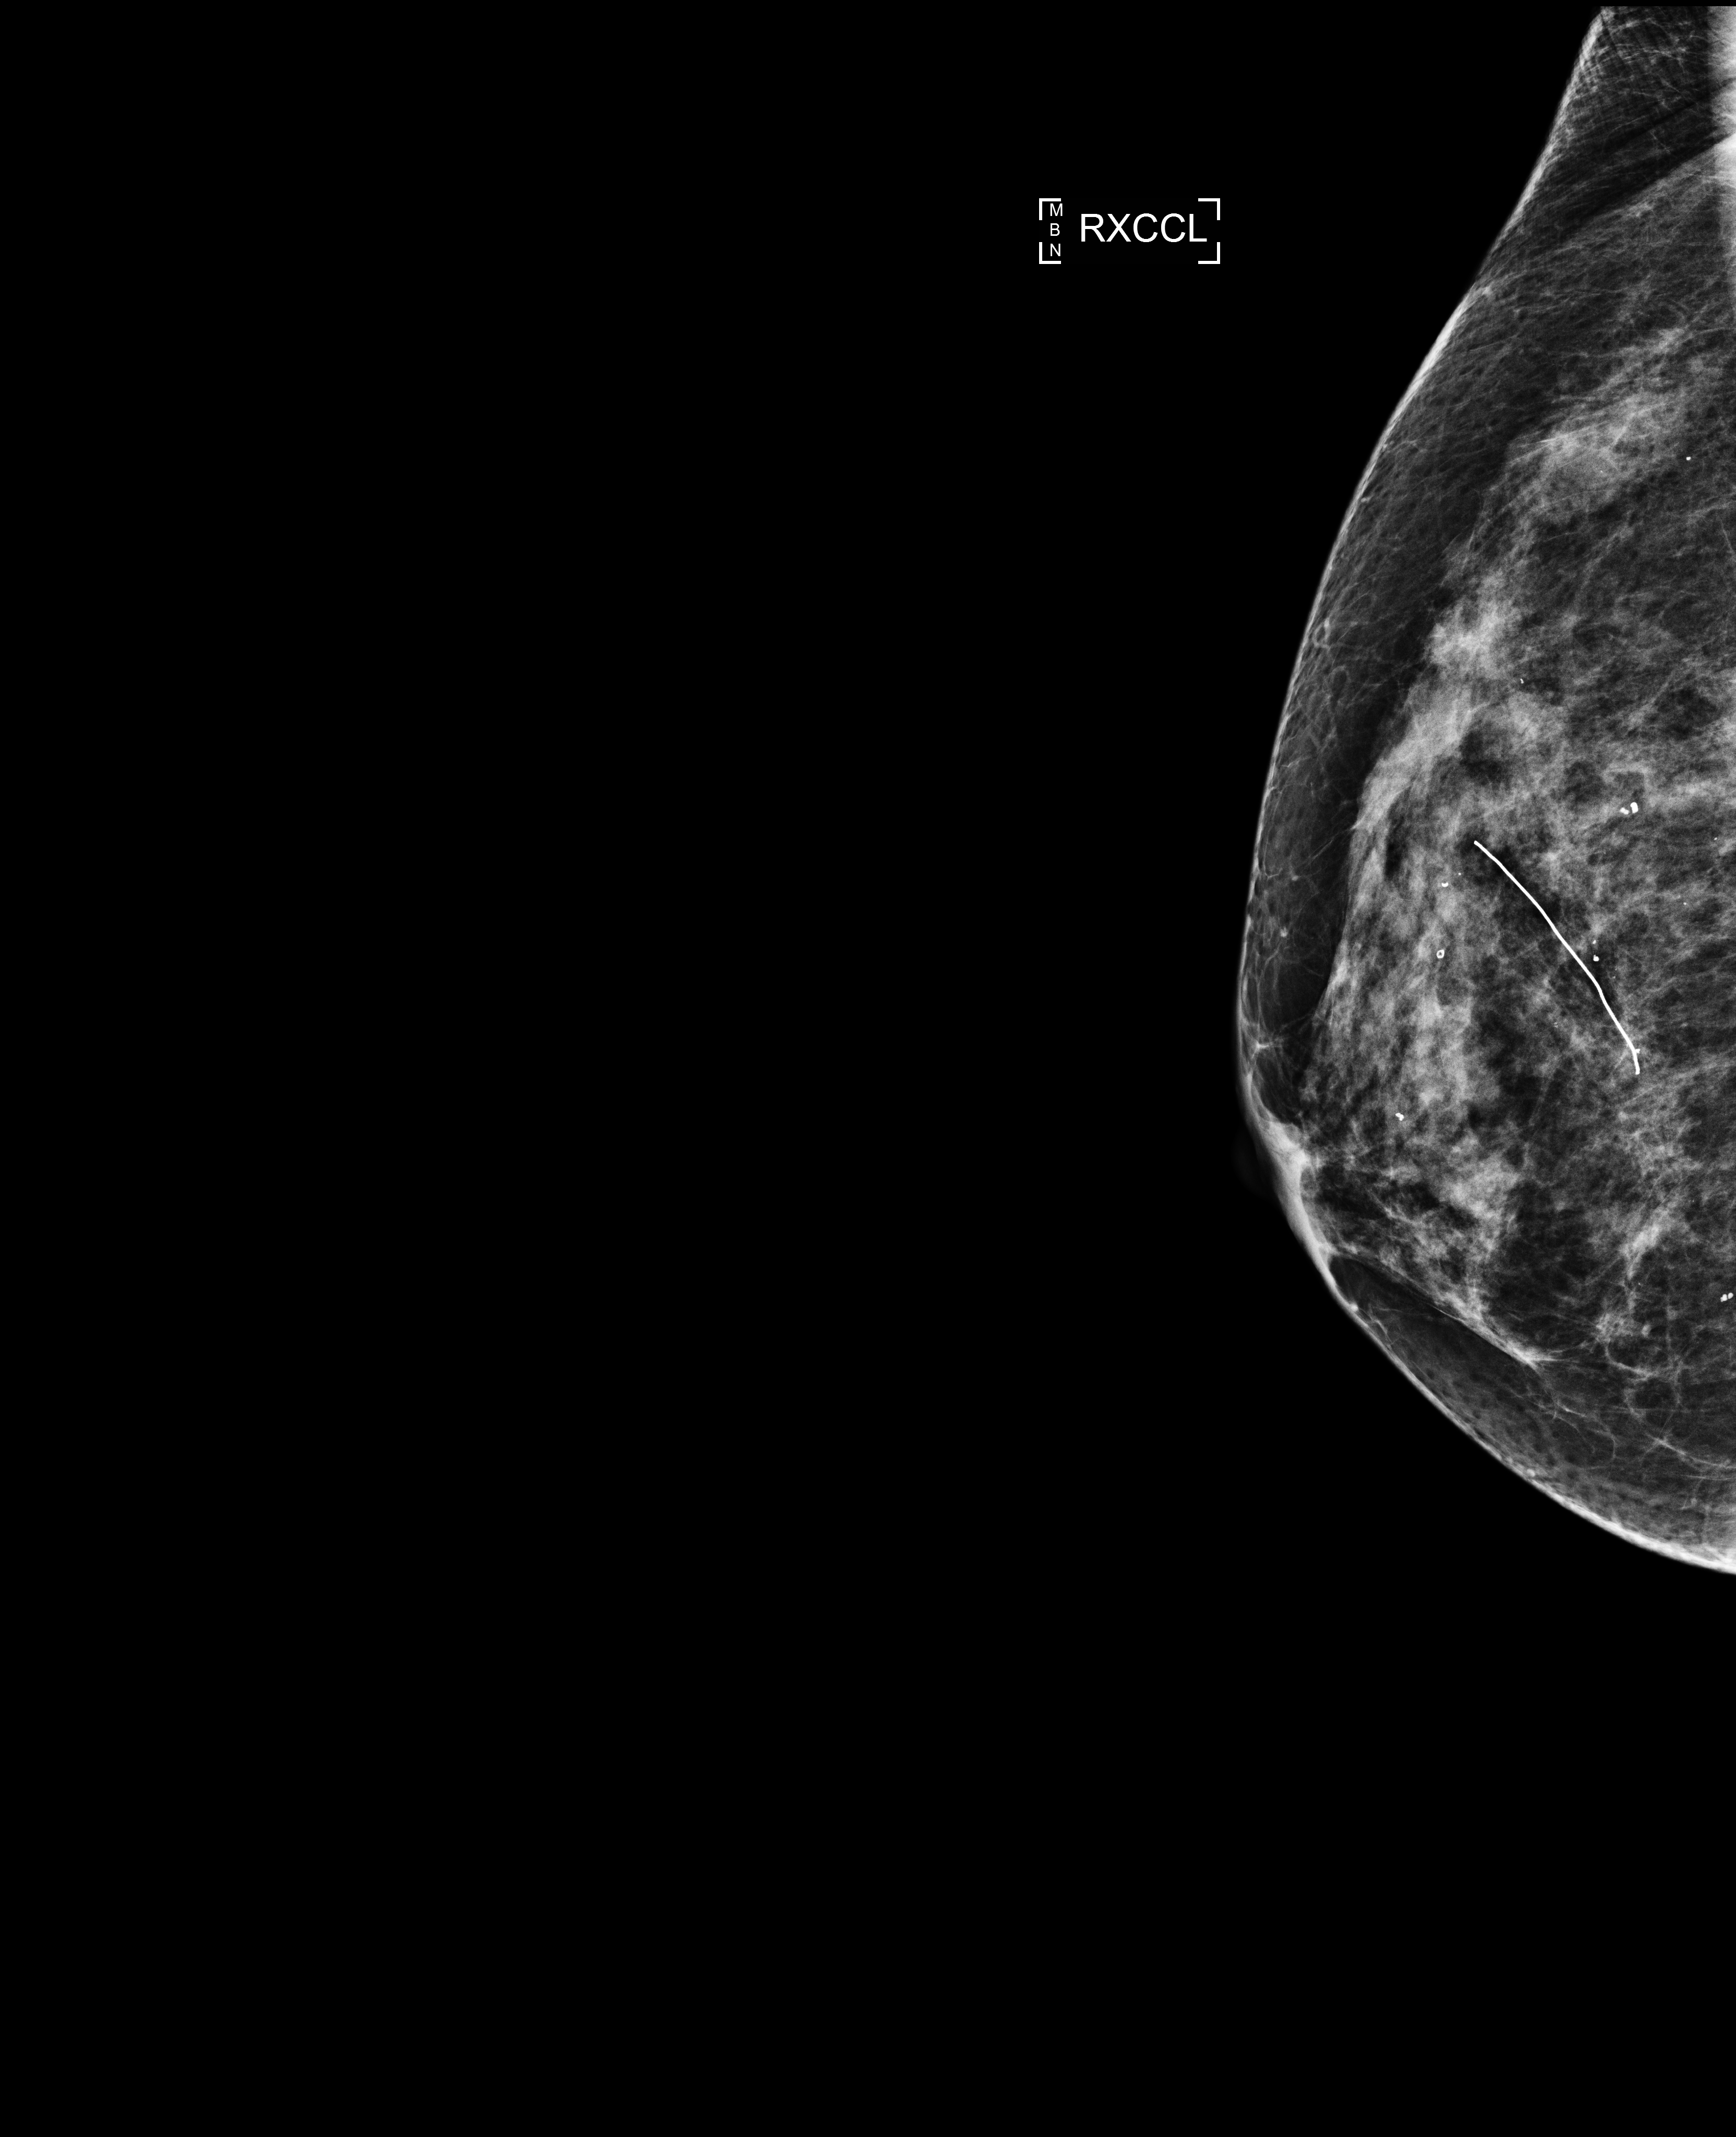
Annual screening mammography examination; compressed breast thickness 46 mm. Female patient, age 75 years.
Image type: full-field digital mammogram. Breast: right. Projection: exaggerated CC view (lateral).